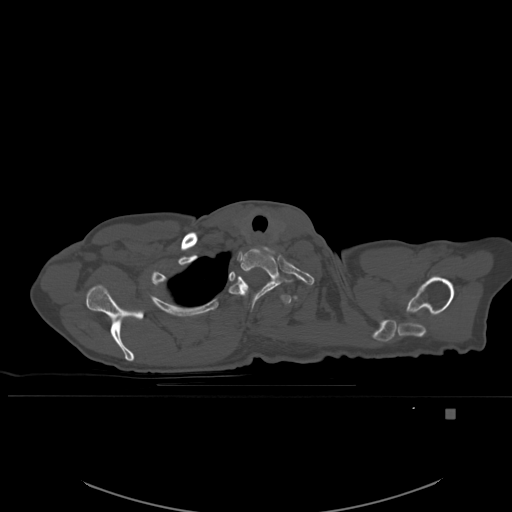
CT including the spine, one axial slice. Bone window (W 1800 / L 400 HU). 1.5 mm slice thickness. 512 × 512 image matrix, field of view 440 × 440 mm. Patient: female, 45 years. Case-level facts recorded for this patient, not image findings: primary cancer: lung.
Annotated regions visible in this slice (semi-automatic segmentation, software-assisted and operator-edited):
- T1 vertebra: bounding box [x1, y1, x2, y2] px = [238, 246, 279, 280]
- T2 vertebra: [229, 276, 290, 311]
- T3 vertebra: [216, 309, 221, 314]